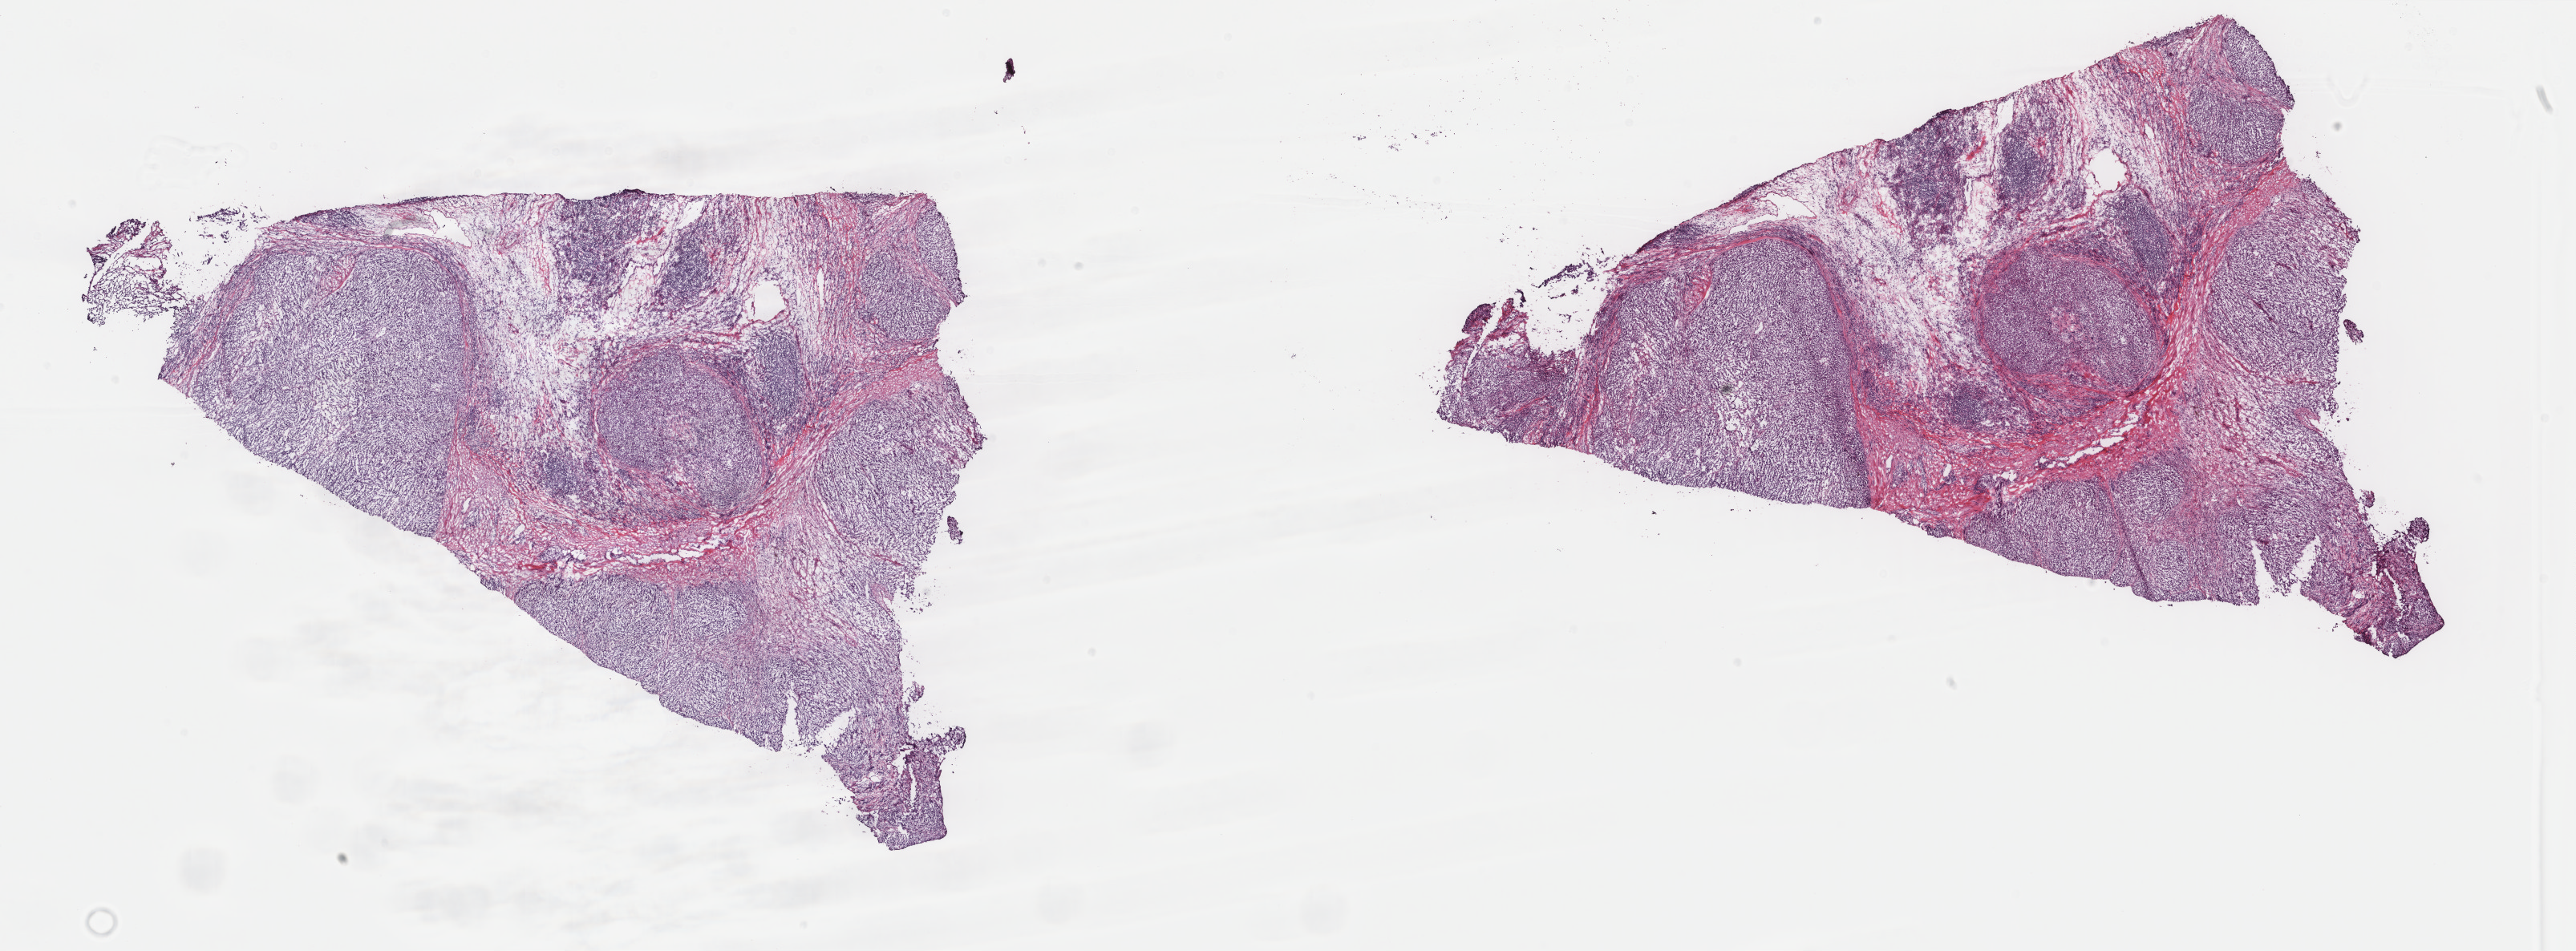
Hematoxylin and eosin (H&E) stained whole-slide image, whole scanned area (about 25.5 x 9.4 mm, from a 40x scan) shown as a low-resolution overview, frozen section from the top of the tissue portion, metastatic tumour sample, sampled site: lymph nodes of axilla or arm. Patient: male, age at initial diagnosis 49 years. Slide review estimates, as recorded: tumour cells 70%, tumour nuclei 70%, normal cells 0%, stromal cells 29%, necrosis 1%. Inflammatory infiltration, as recorded: lymphocyte infiltration 6%, monocyte infiltration 1%, neutrophil infiltration 1%.
- this section: metastatic tumour tissue
- patient diagnosis: Malignant melanoma, NOS